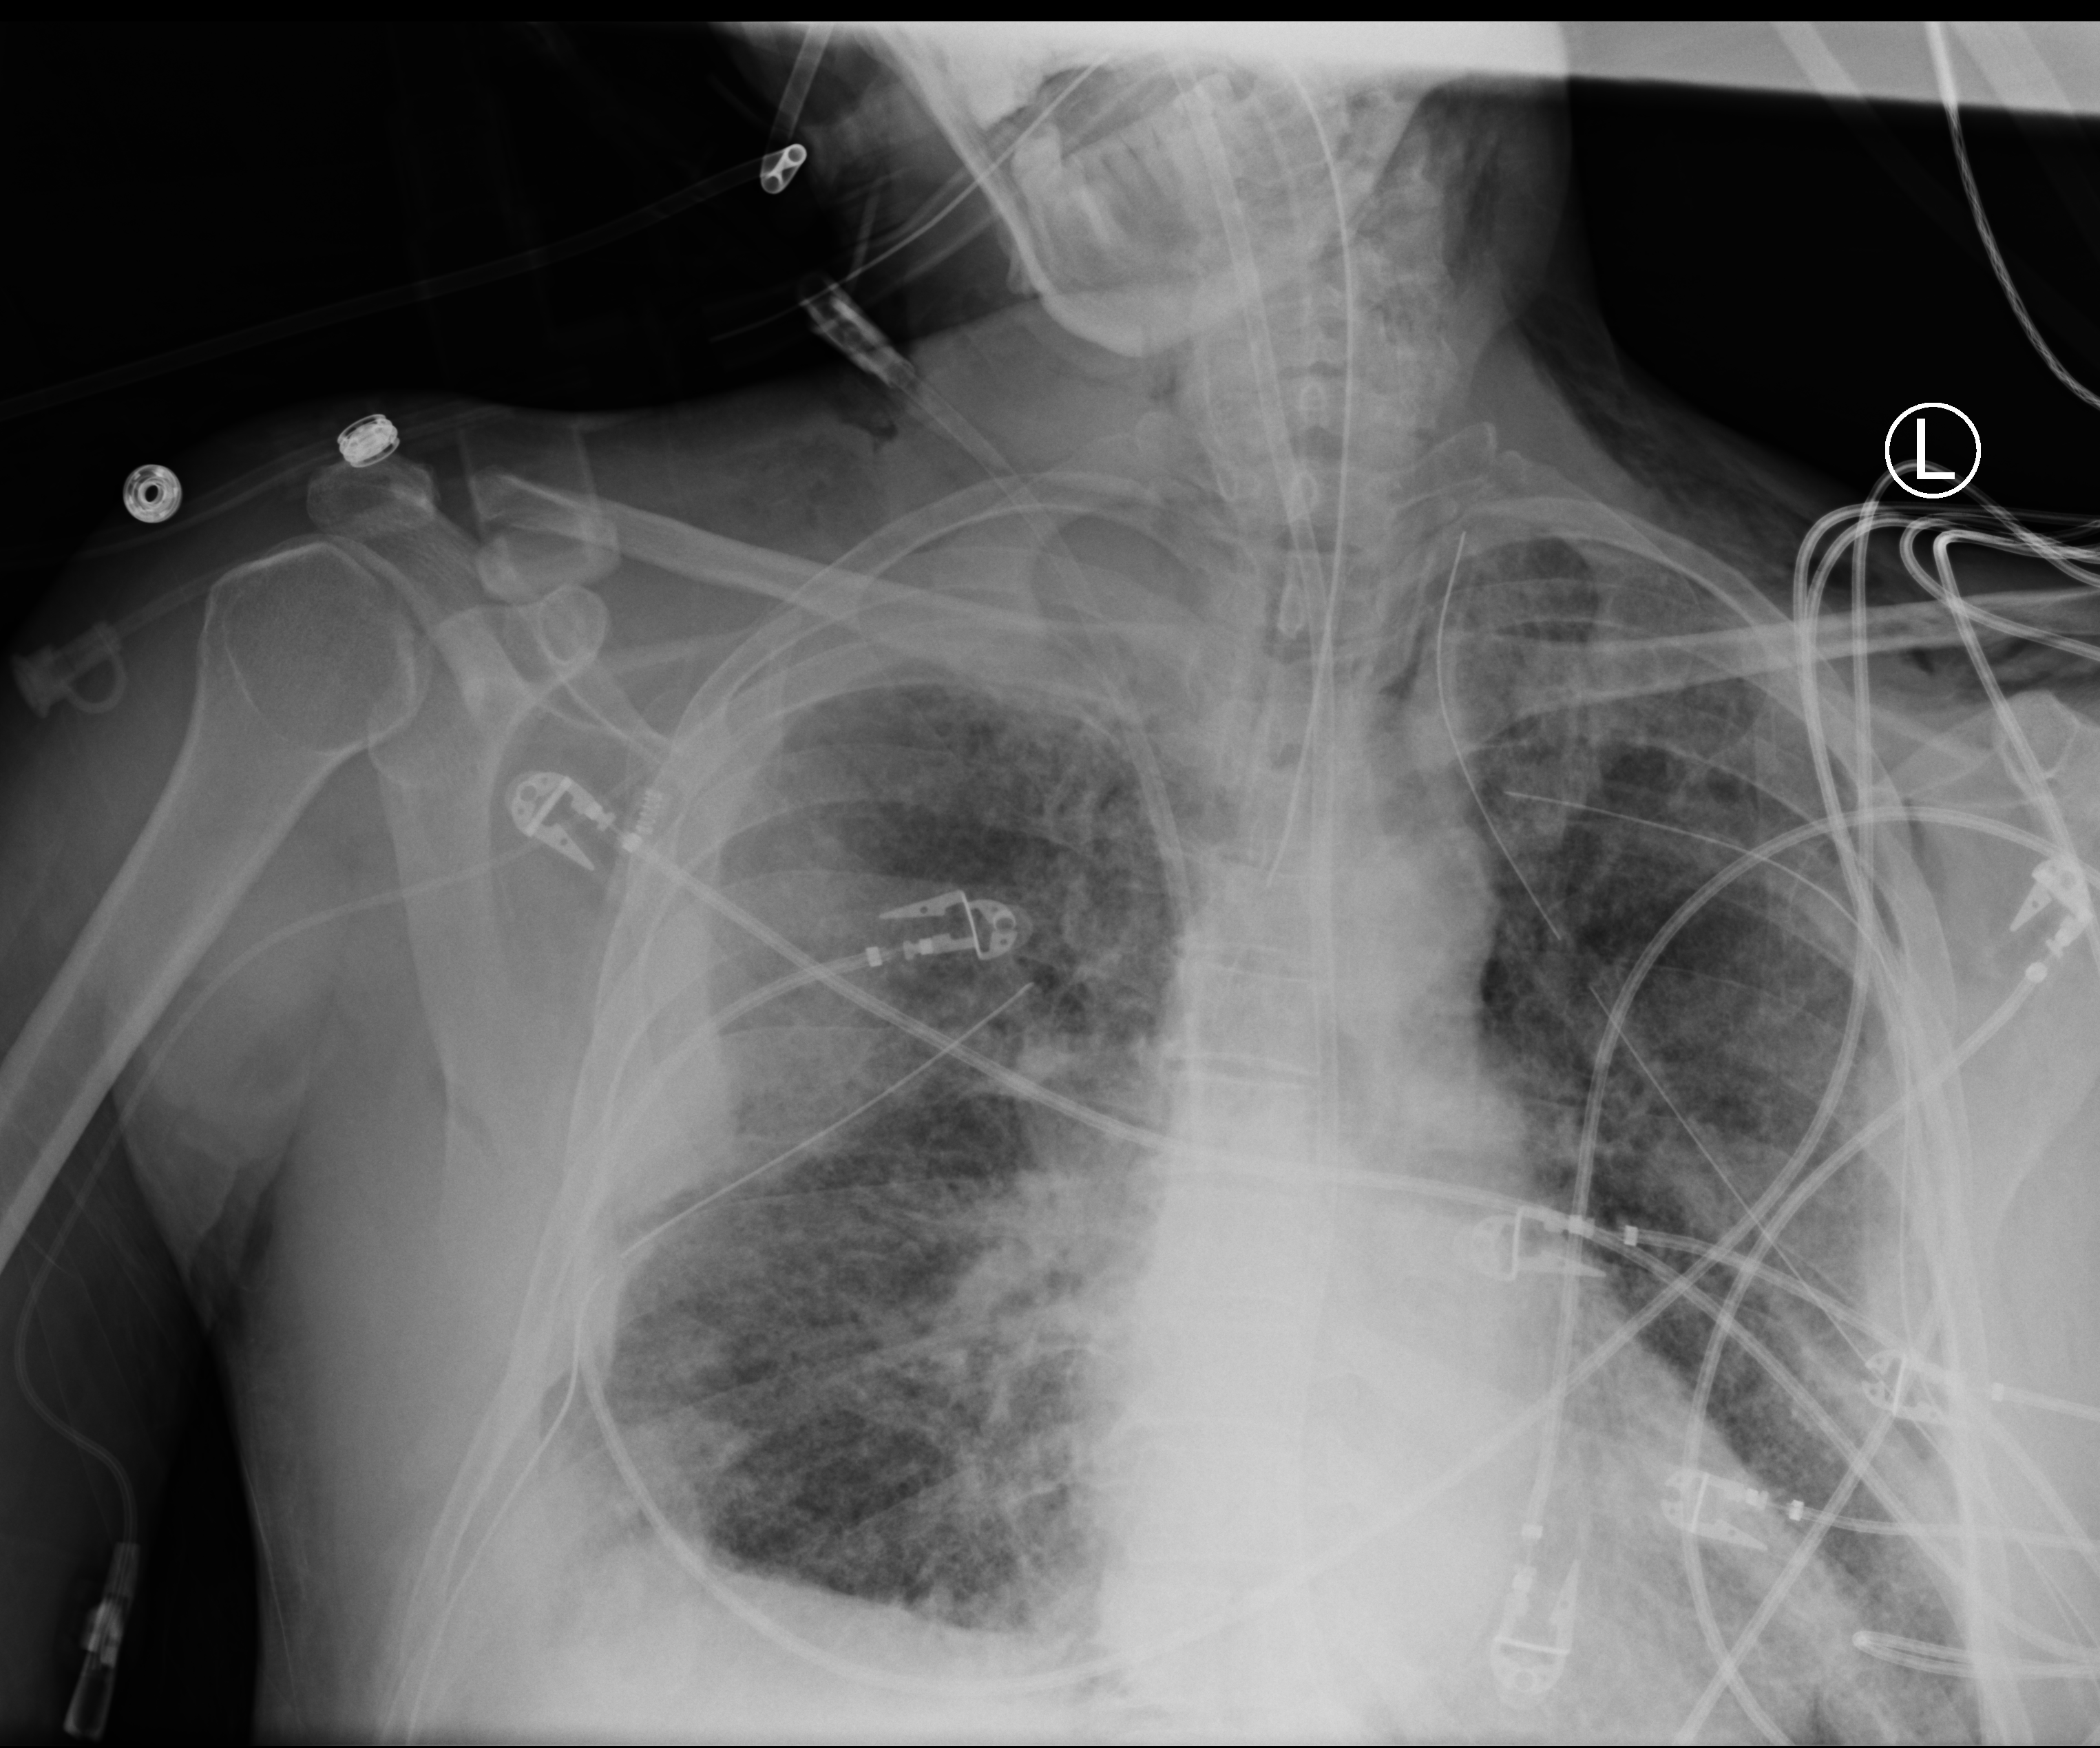
Bedside chest radiograph (computed radiography); anteroposterior (AP) projection. Male patient hospitalised with COVID-19, age 18–59 years.
Admission-level facts for this patient (not findings on this image; timing relative to this image not recorded):
- mechanically ventilated during this hospital stay: yes
- admitted to intensive care during this hospital stay: yes